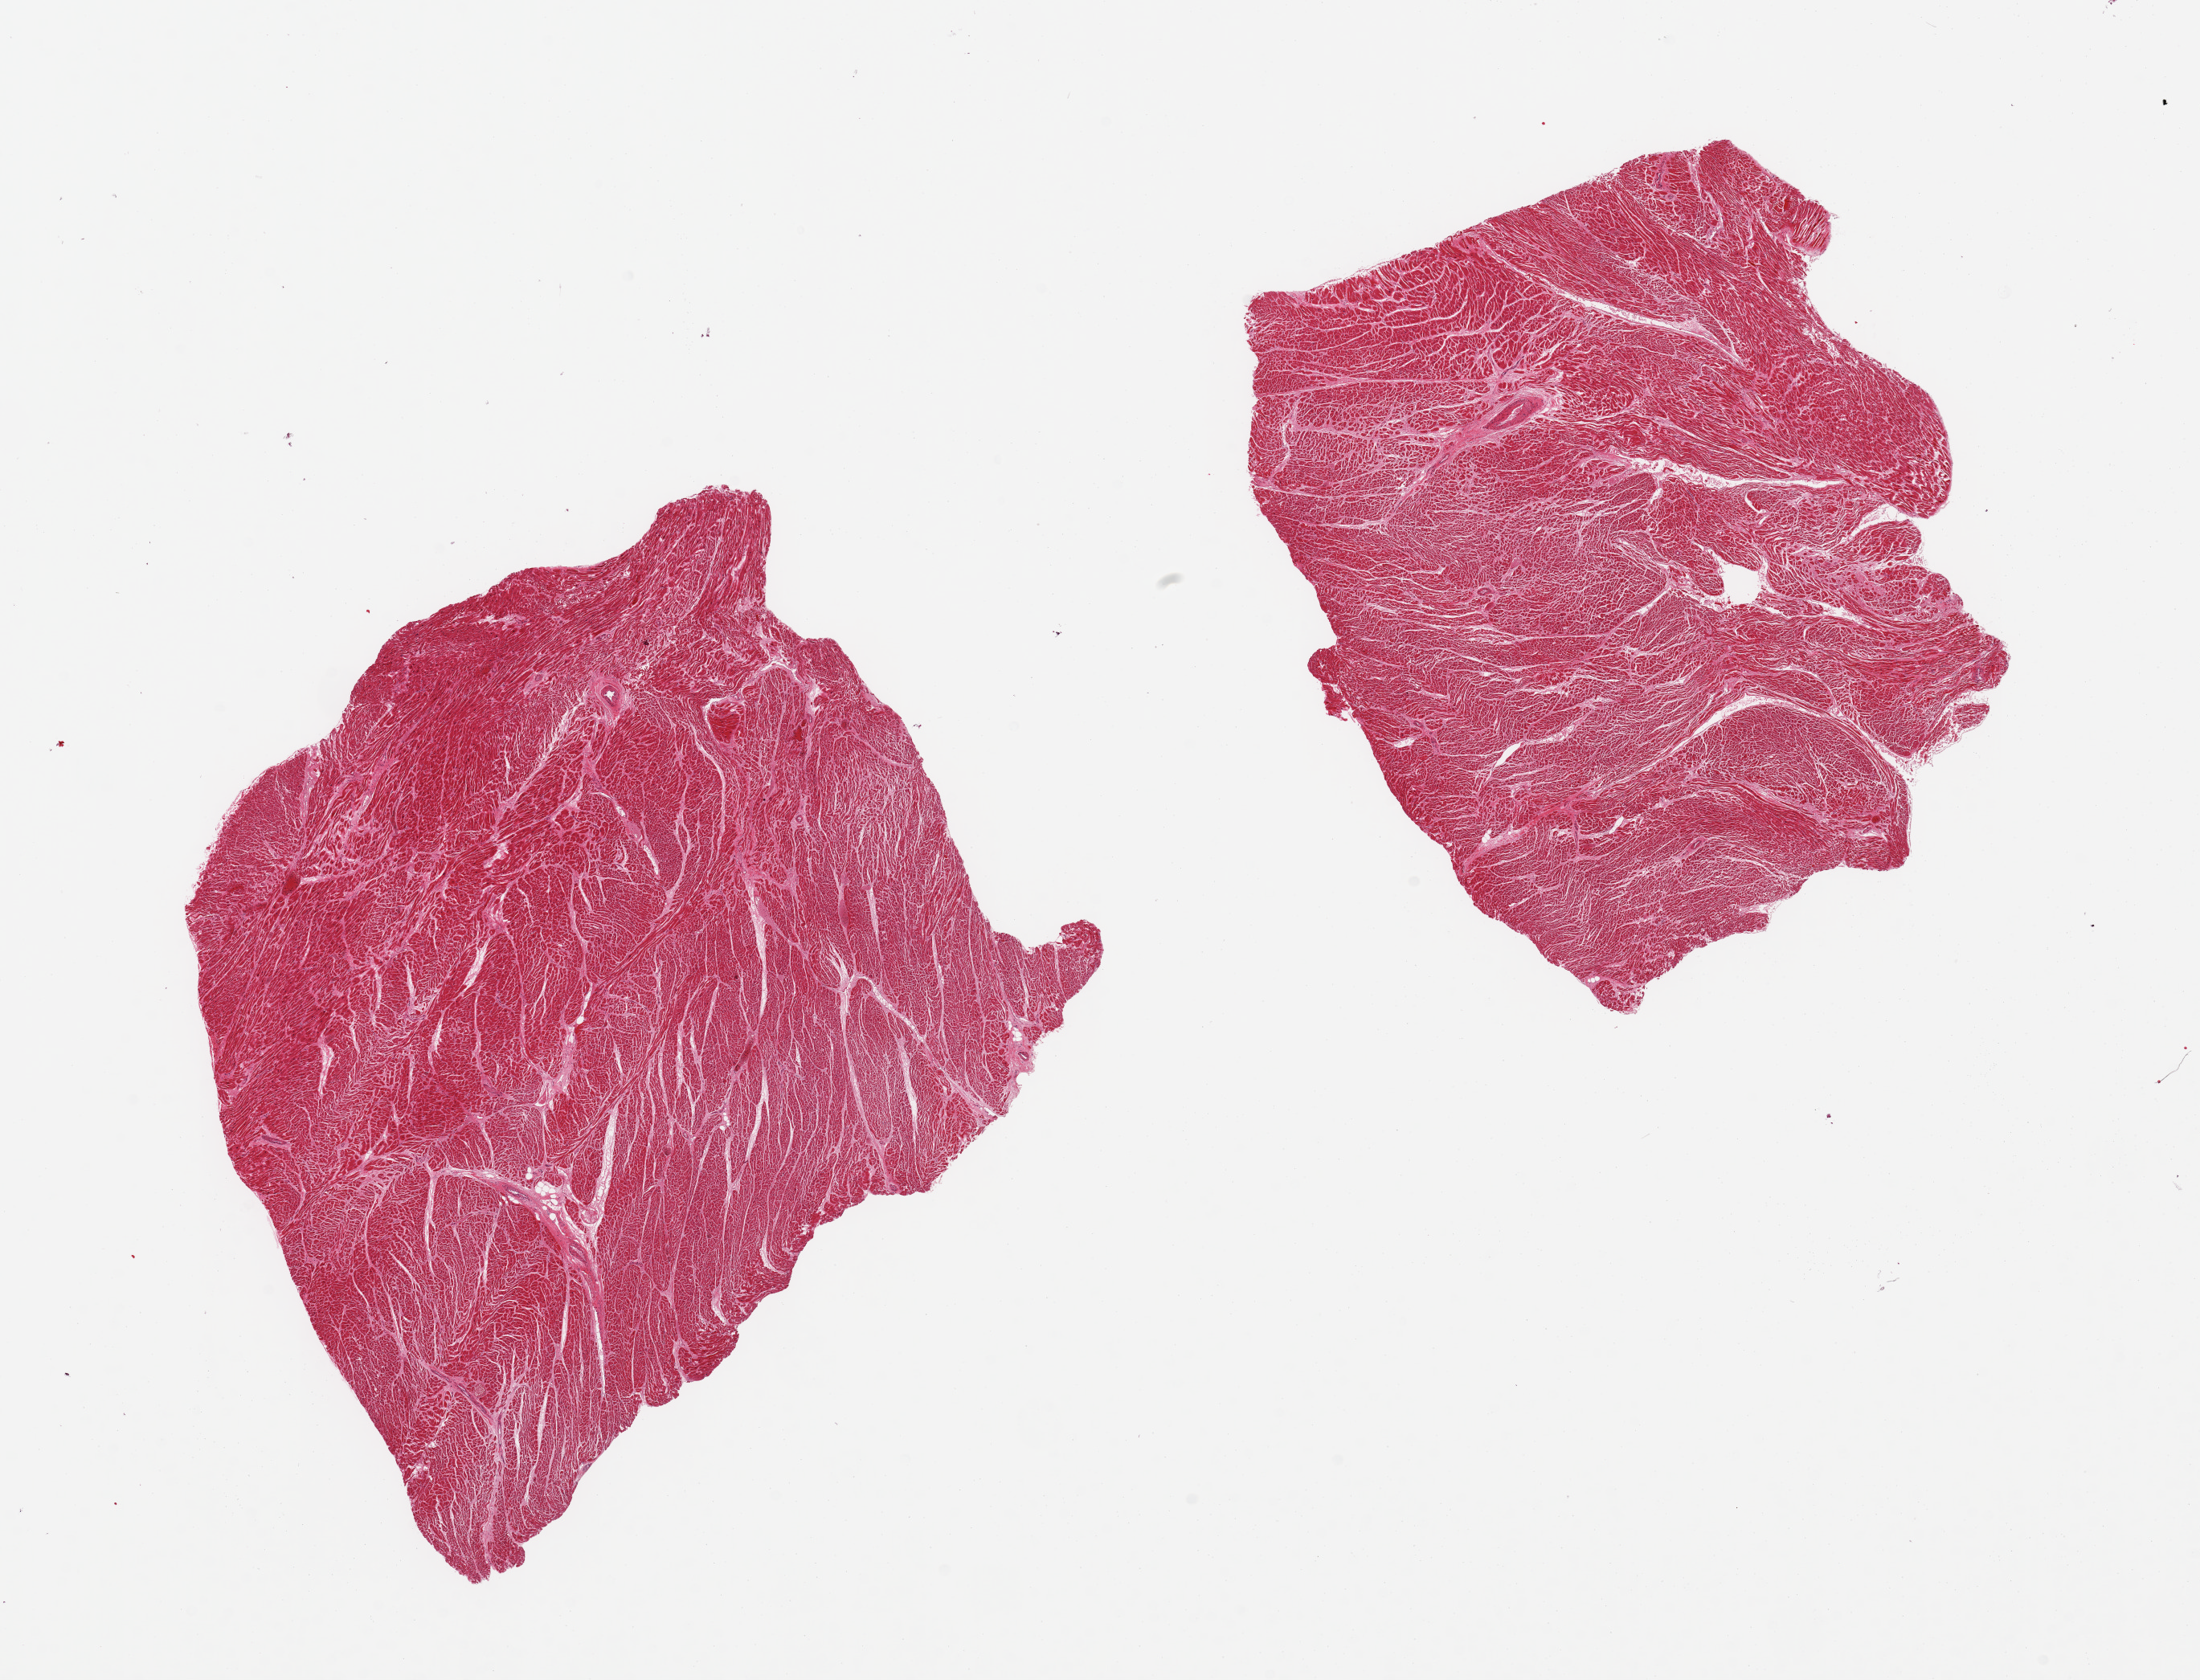
Haematoxylin and eosin whole-slide image — whole scanned area (about 21.7 x 16.5 mm, slide scanned at 20x) shown as a low-resolution overview, PAXgene-fixed paraffin-embedded (PFPE) section, target tissue: heart, donor tissue sample. Donor: male.
Pathologist's review note for this sample: 2 pieces, myocyte hypertrophy.